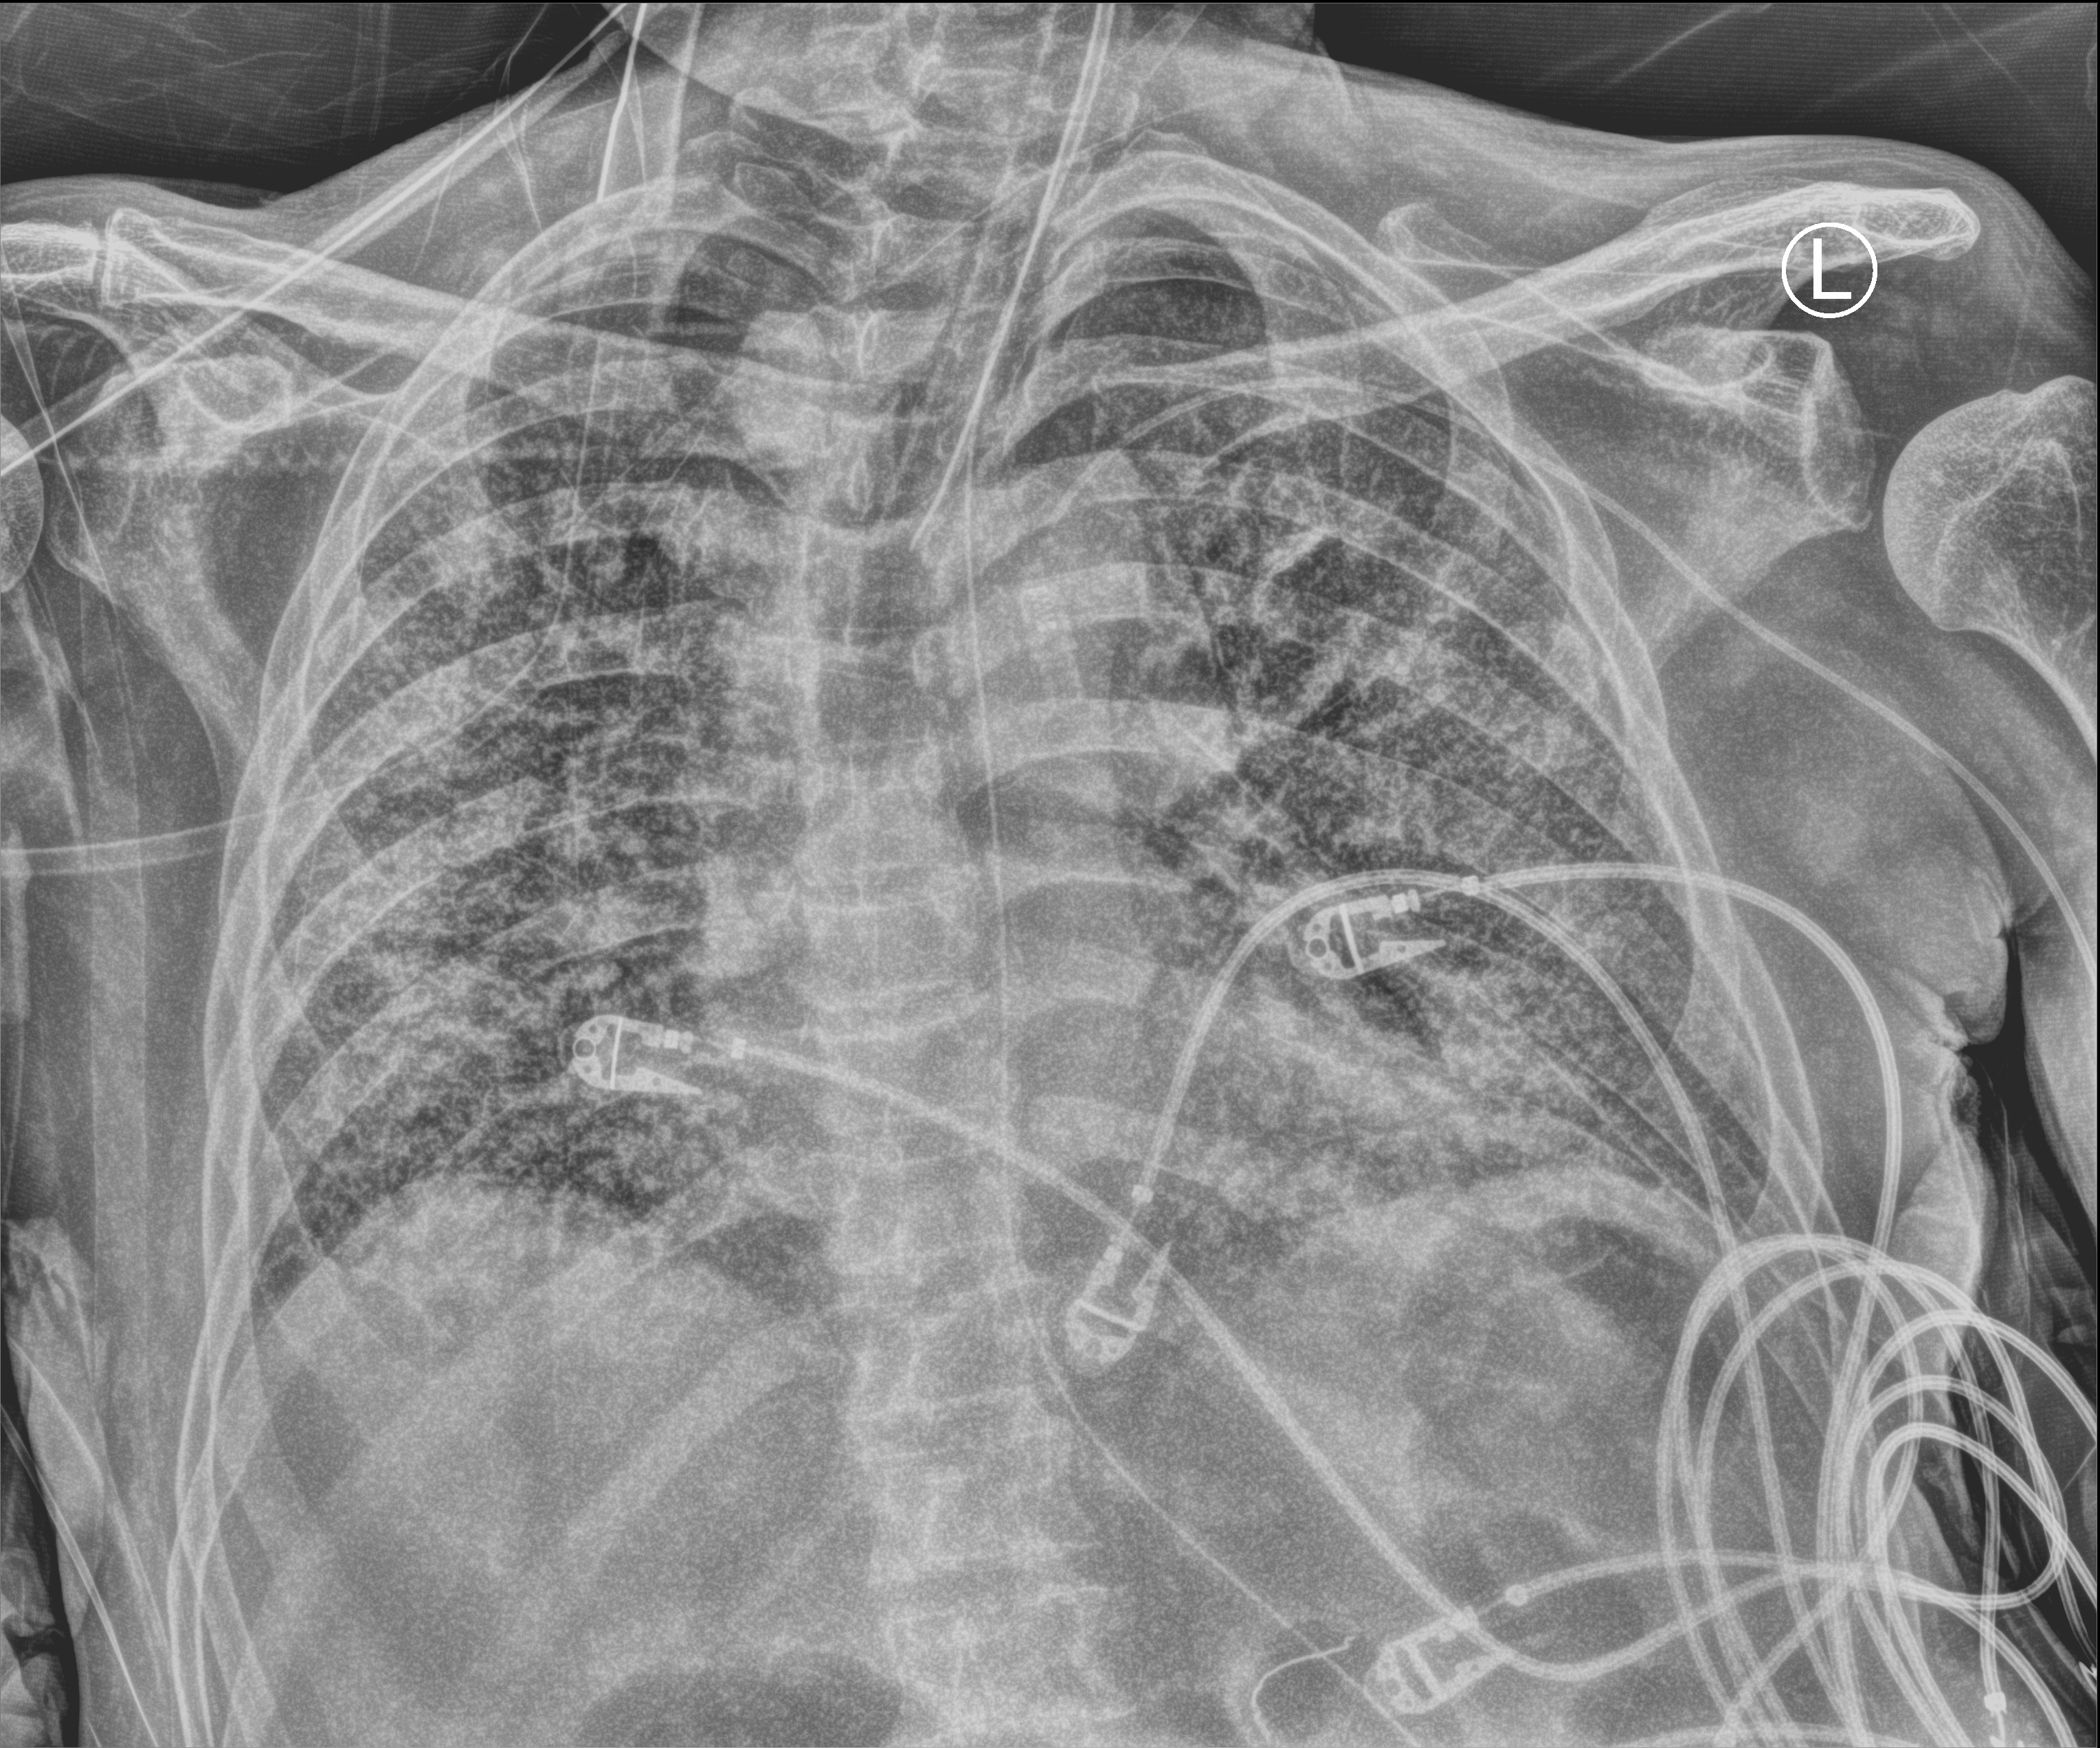
Chest X-ray (portable). Patient hospitalised with COVID-19; male, aged 60–74 years.
Admission-level facts for this patient (not findings on this image; timing relative to this image not recorded): admitted to intensive care during this hospital stay: yes; length of hospital stay: 54 days; mechanically ventilated during this hospital stay: yes.